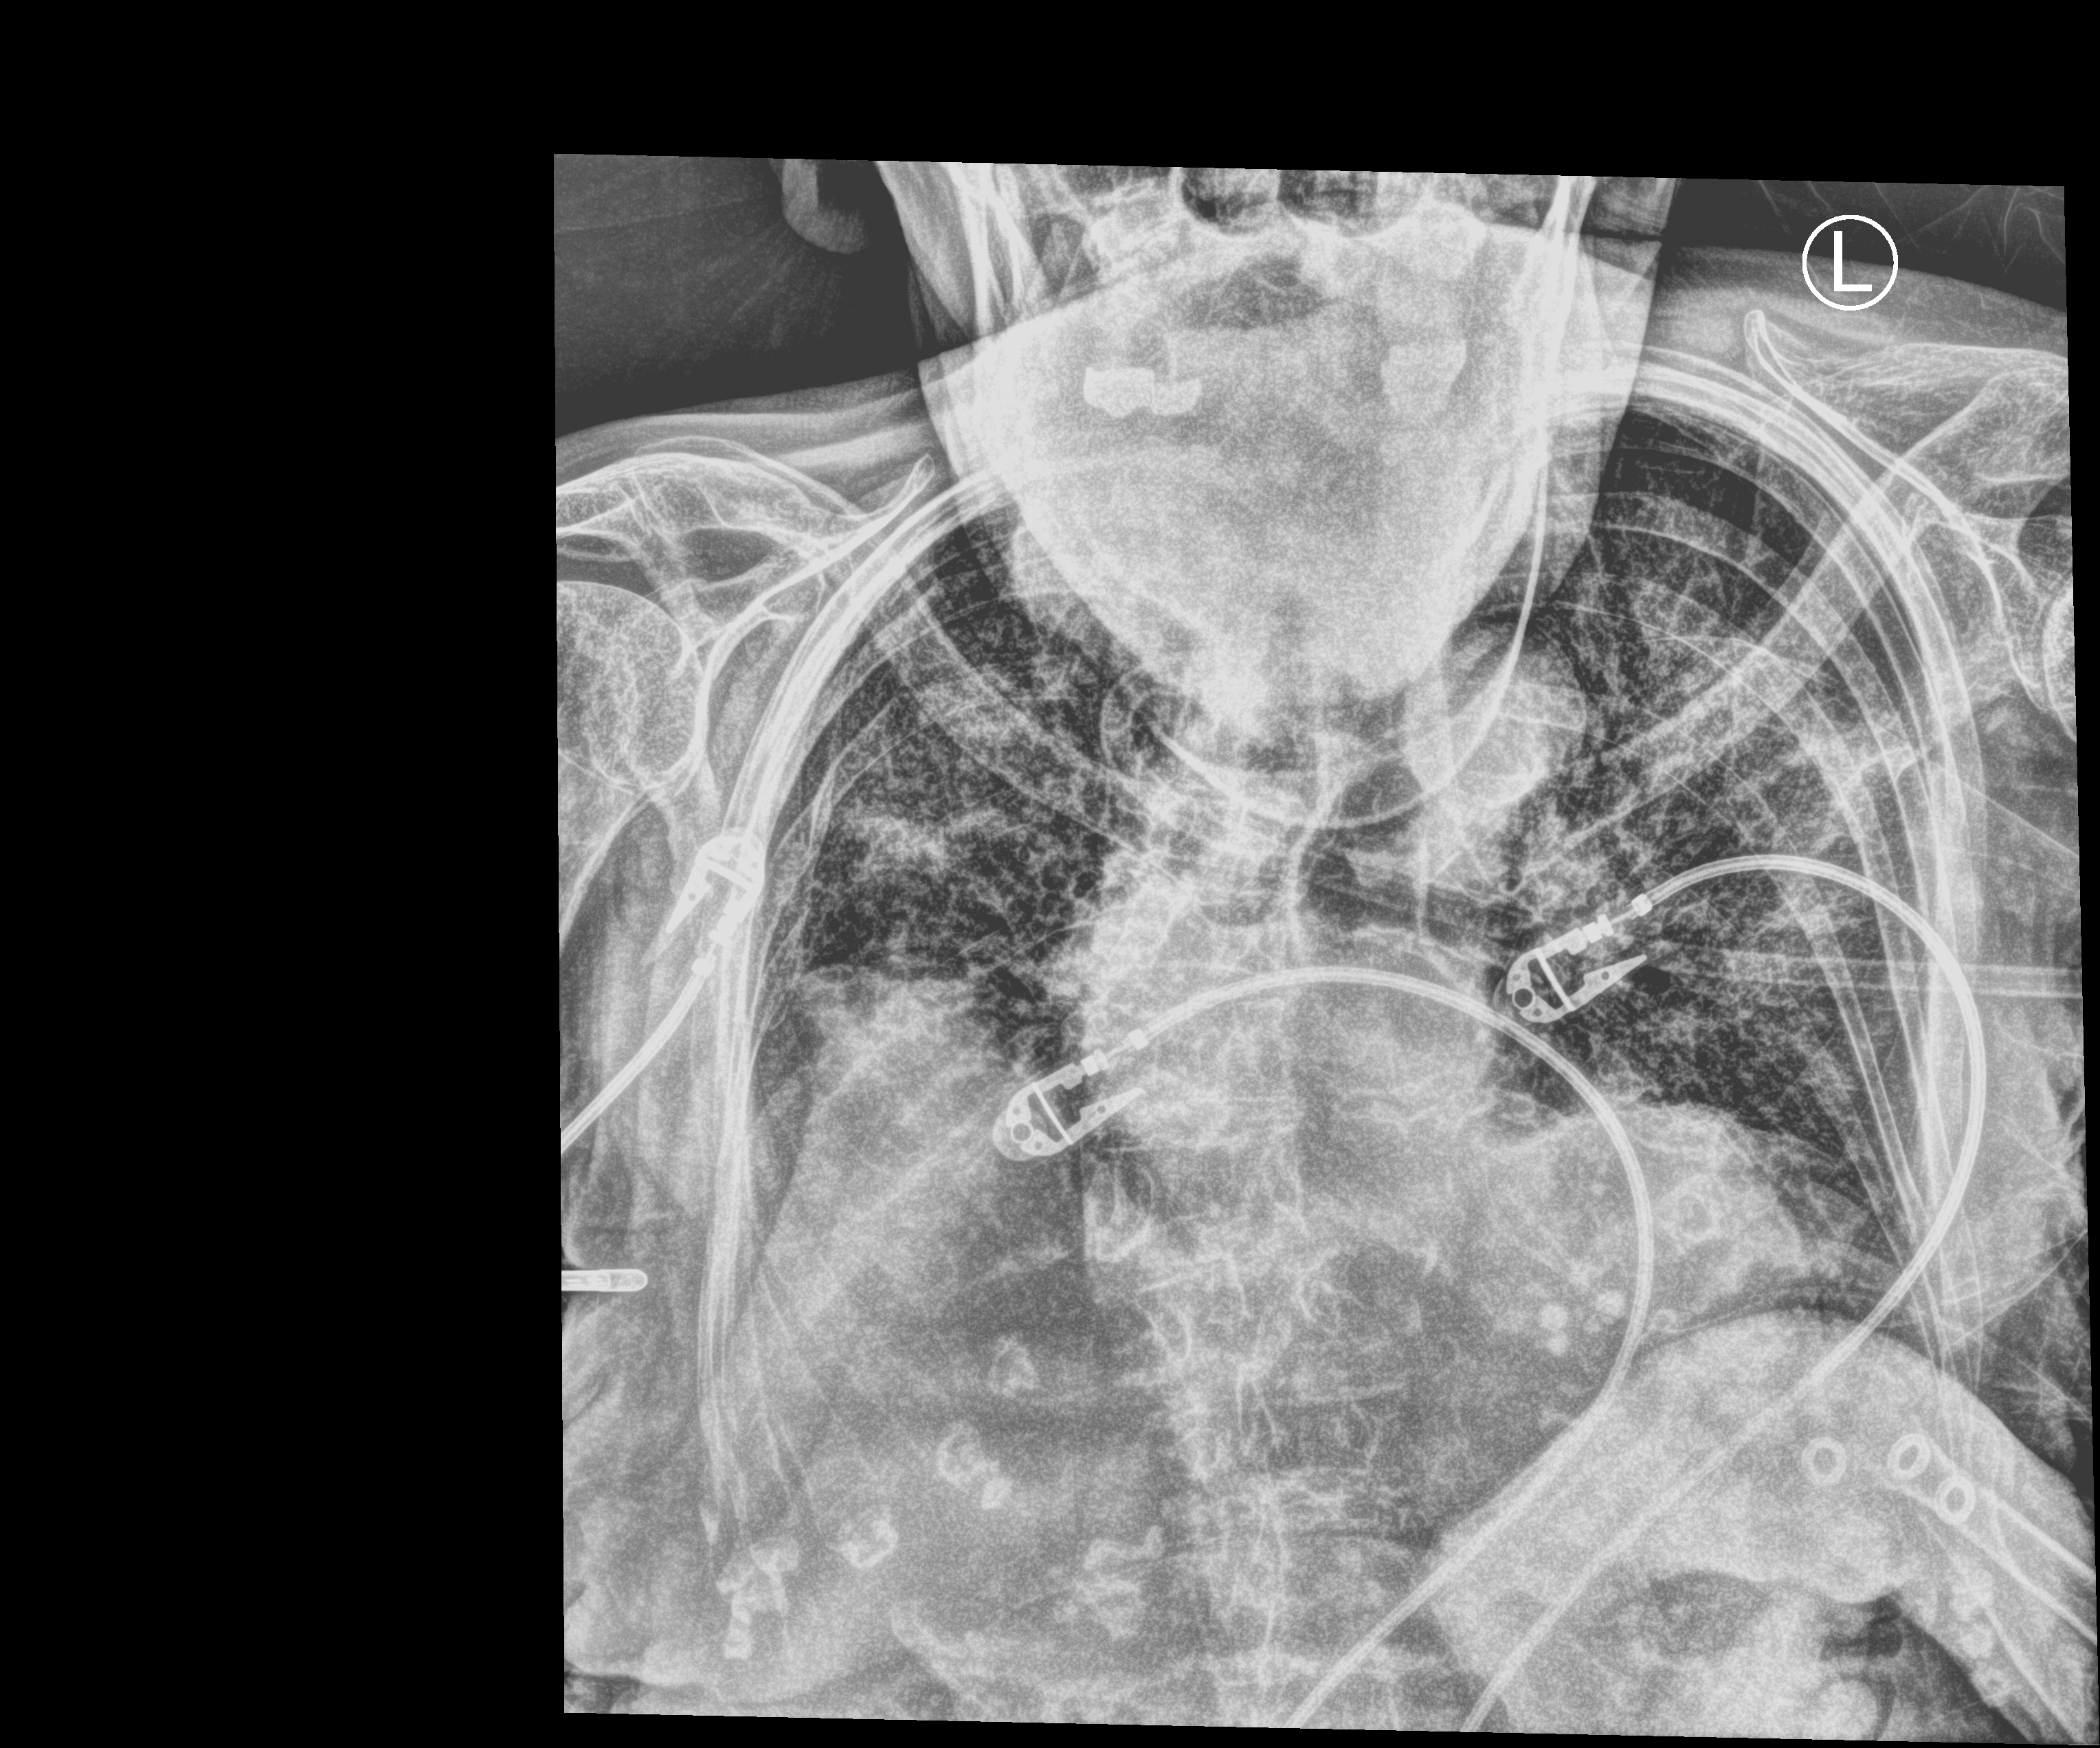
Bedside chest radiograph (computed radiography), anteroposterior (AP) projection. Patient hospitalised with COVID-19; female, aged 75–90 years.
Hospital-stay facts (about this admission, not read from this image; timing relative to this image not recorded): mechanically ventilated during this hospital stay: no.